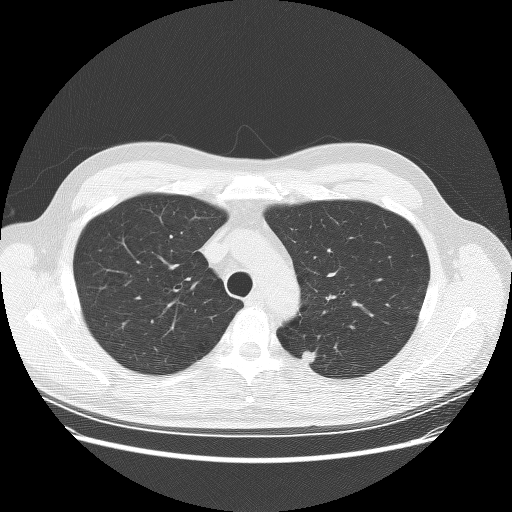
Low-dose screening chest CT, one axial slice. Slice 201 of 253 in the series (ordered by position). Lung window (W 1500 / L -600 HU). 512 × 512 image matrix, field of view 370 × 370 mm.
Structures marked on this image (manually delineated by an expert):
- lesion 2 (nodule): bounding box <302,351,317,364> (left, top, right, bottom; pixels)